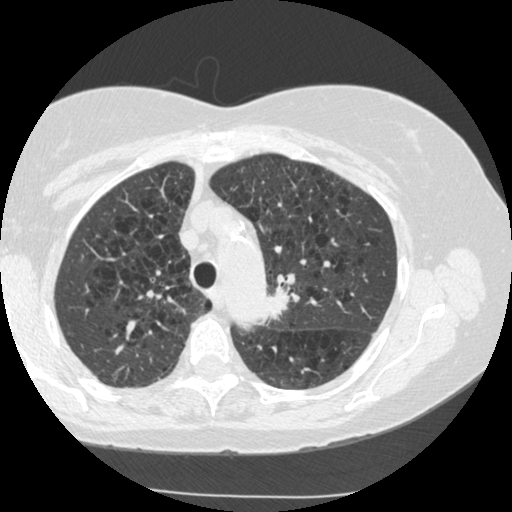
Chest CT (low-dose screening protocol), one axial image, second screening round (one year after baseline), lung window (W 1500 / L -600 HU), 1.25 mm slice thickness, standard (soft-tissue) reconstruction kernel (STANDARD), 120 kVp. Female participant, aged 70 years at enrolment. Current smoker at enrolment.
Lesion marked by an expert reader, bounding box (x1, y1, x2, y2) in pixels: (240, 269, 303, 333). Screening reader's record for this exam (one nodule recorded; not confirmed to be the boxed lesion): non-calcified nodule or mass ≥4 mm, left upper lobe, 15 × 13 mm, spiculated (stellate) margins, soft tissue attenuation, pre-existing on the prior screen: yes; interval growth: yes.